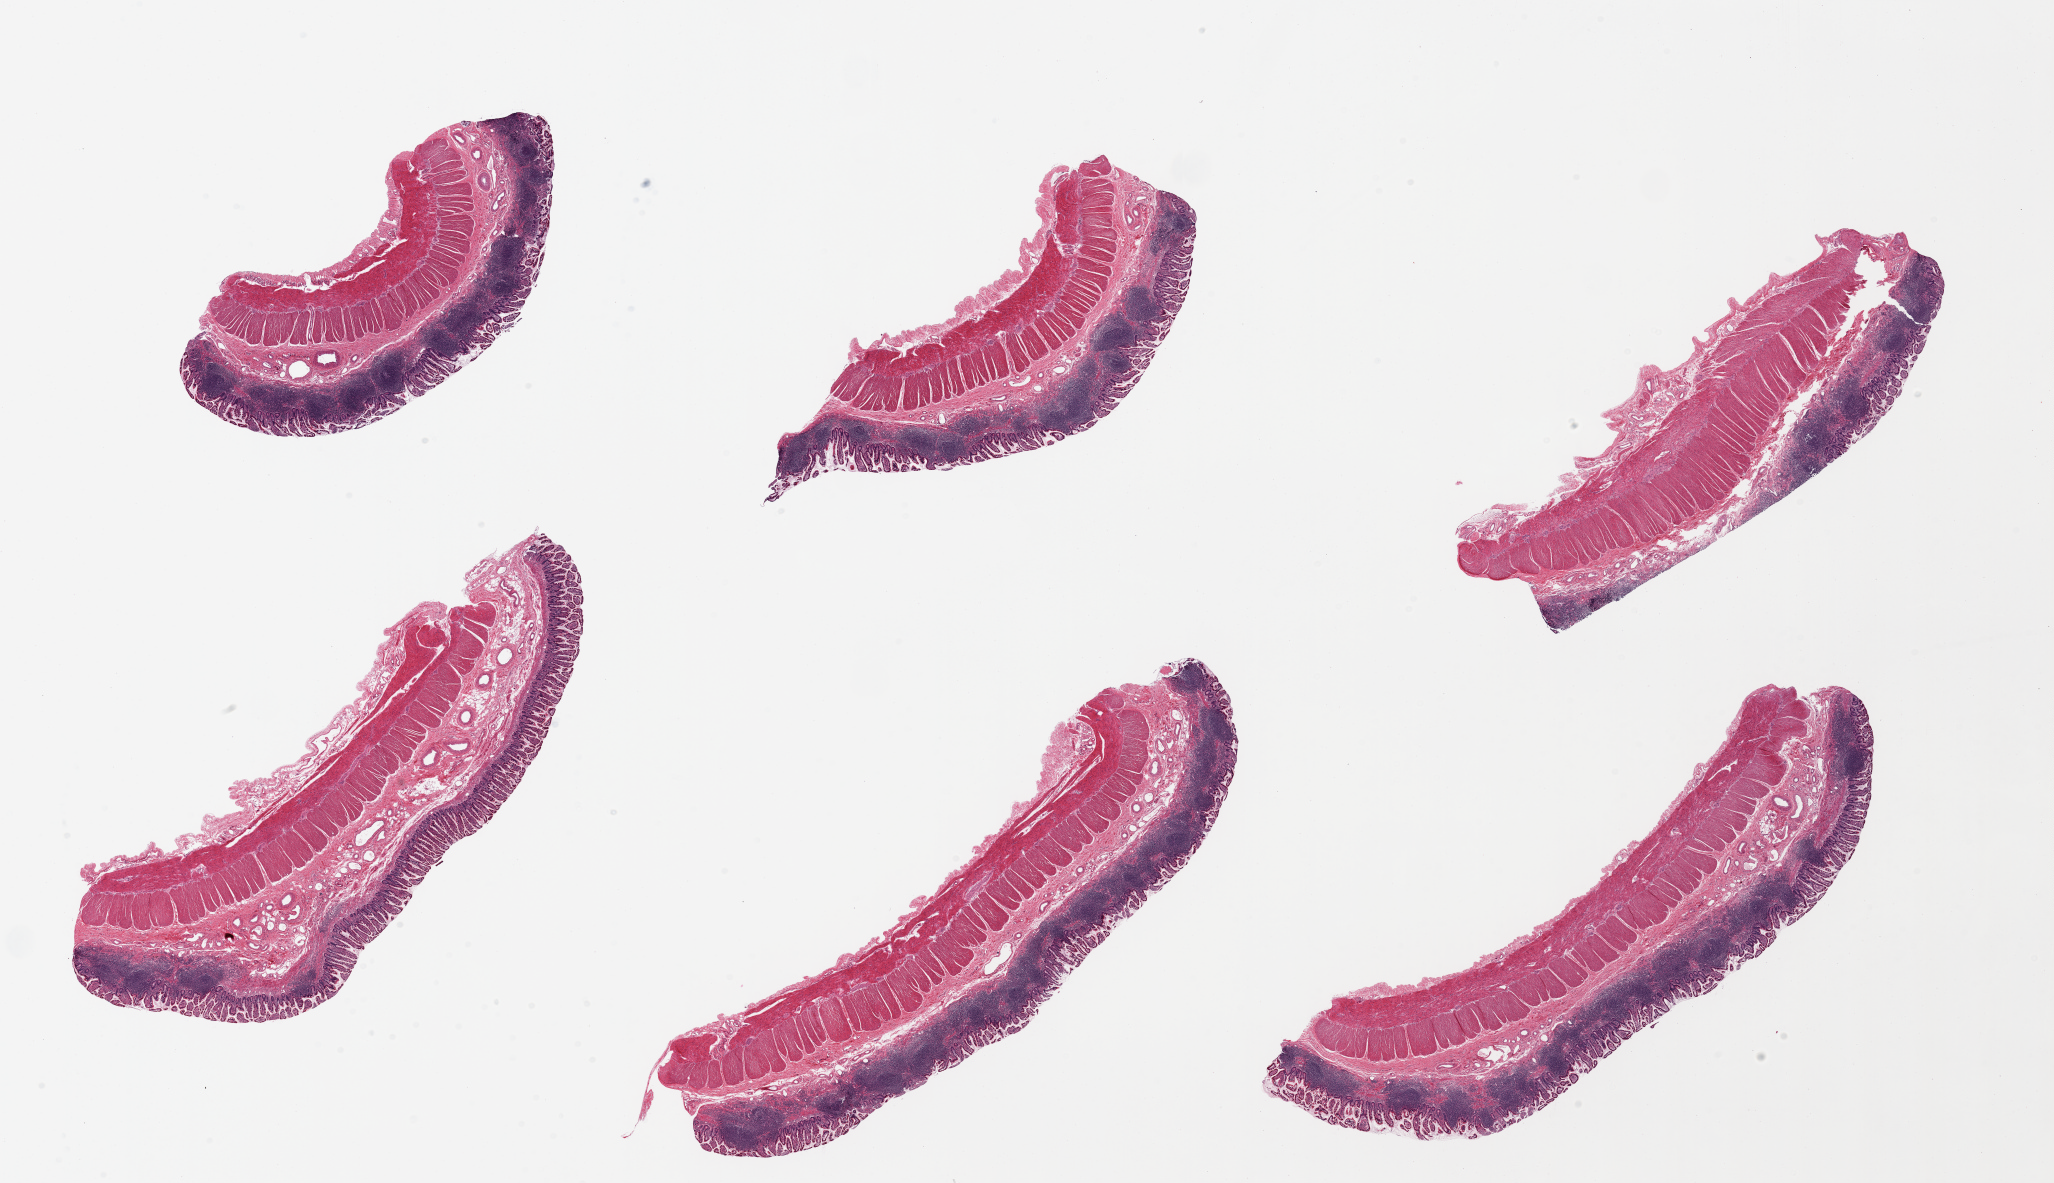
Digitized haematoxylin and eosin-stained section — a low-resolution overview of the entire scanned area, about 32.5 x 18.7 mm (from a 20x scan), PAXgene-fixed paraffin-embedded (PFPE) section, sampled site (target tissue): ileum, tissue donor sample. Donor sex: male.
Pathologist's review note for this sample: 6 pieces. All with abundant mucosal lymphoid tissue [Peyer patches]. All also have muscularis propria (not target).